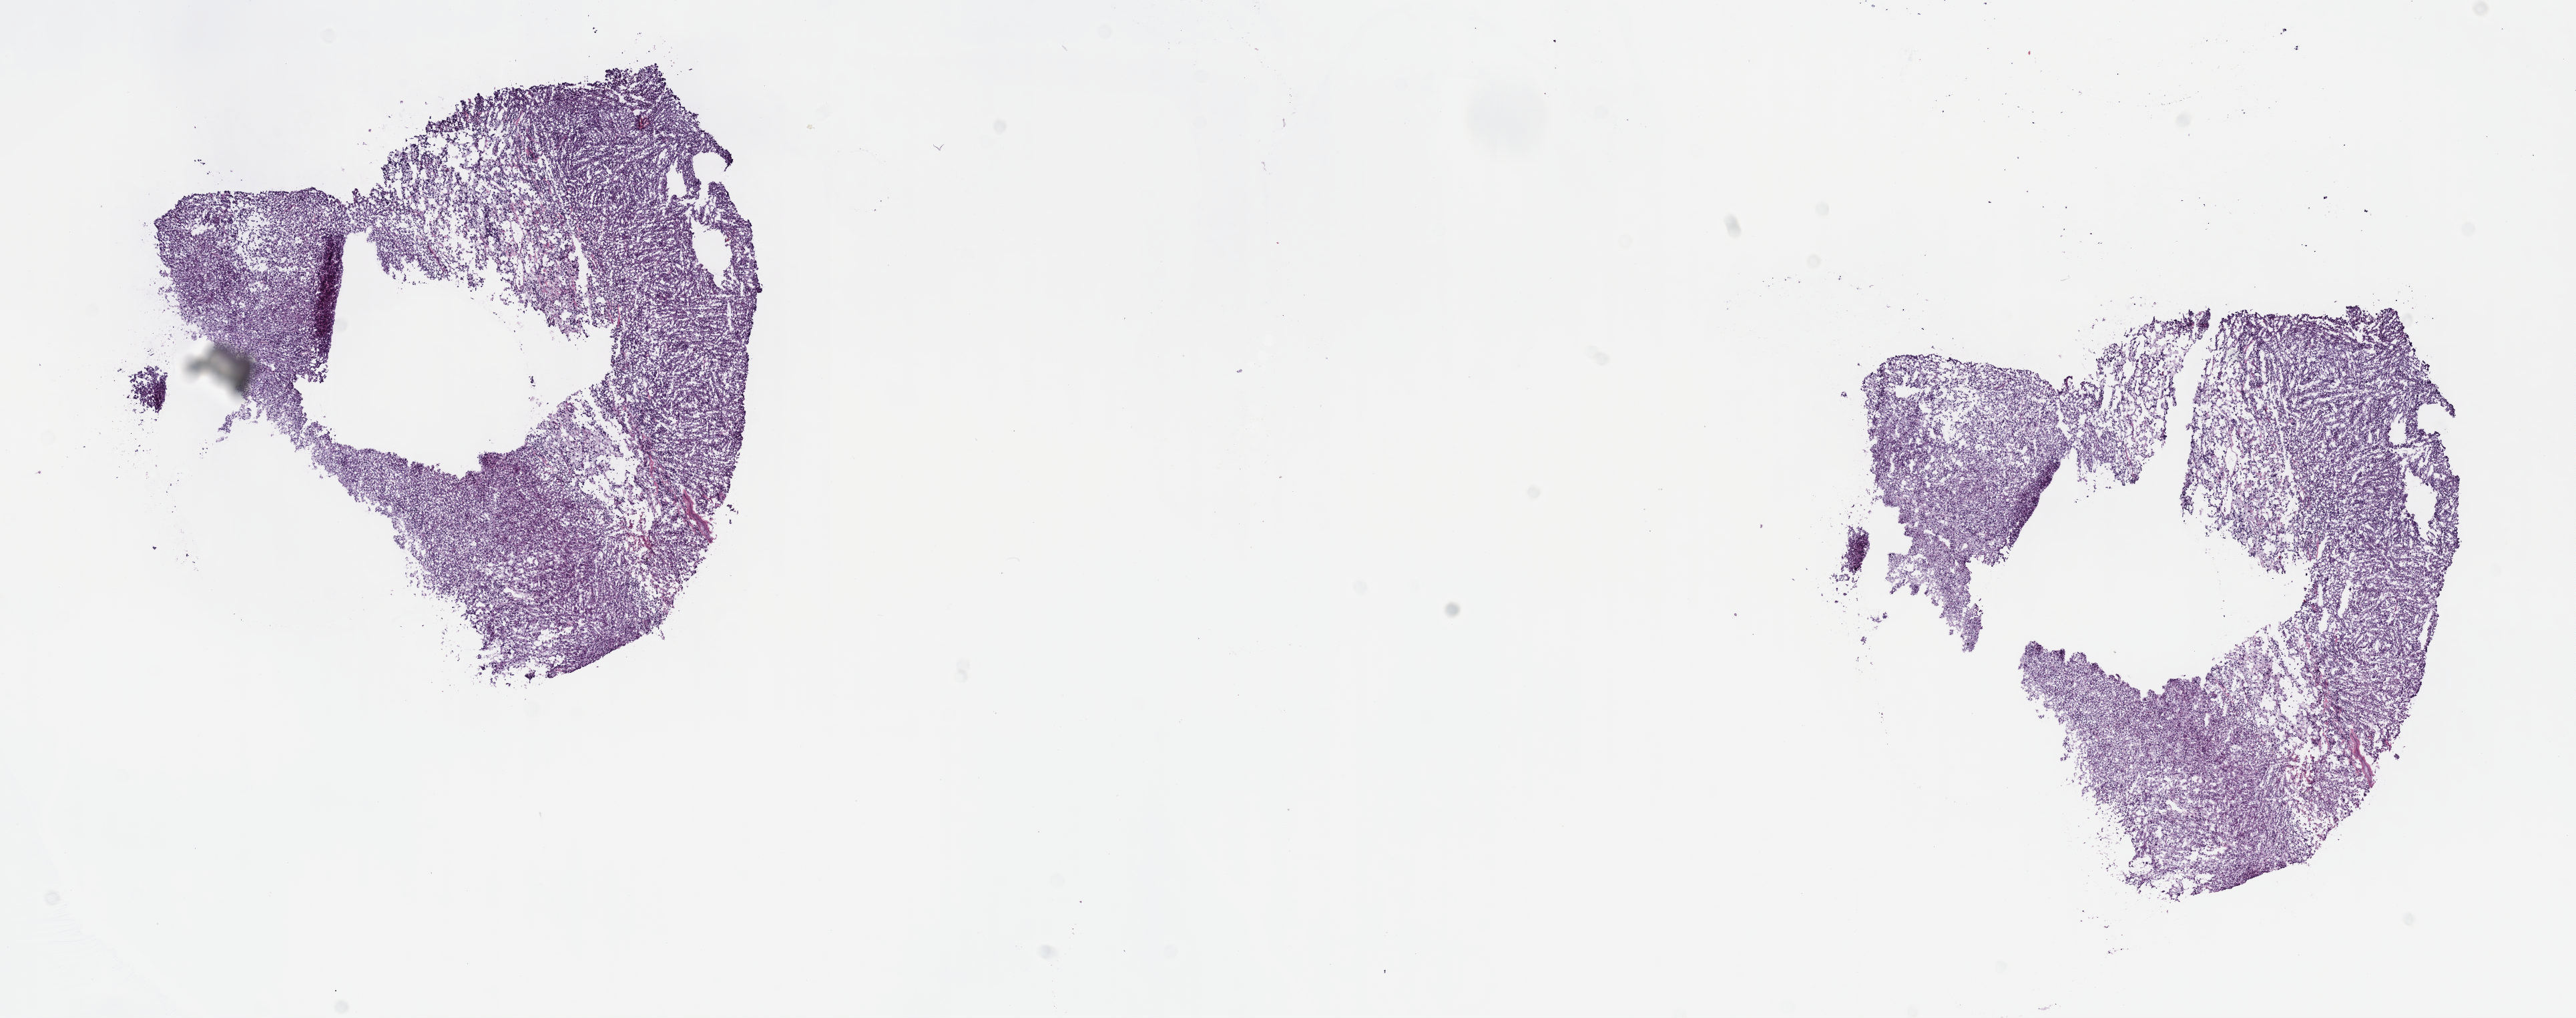
Digitized H&E-stained tissue section (whole slide), shown as a low-resolution overview of the whole scanned area (about 15.6 x 6.2 mm, acquisition: 40x scan). Frozen section. Primary tumour sample from the kidney. Male, age 38 years at initial diagnosis. Pathologist review of this section (percent, as recorded): tumour cells 65%, tumour nuclei 70%, normal cells 0%, stromal cells 30%, necrosis 5%. Infiltration values recorded for this section: lymphocyte infiltration 0%, monocyte infiltration 10%, neutrophil infiltration 0%.
AJCC pathologic stage: III (7th edition). Diagnosis: Papillary adenocarcinoma, NOS.